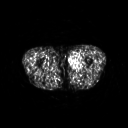
FDG PET of an extremity soft-tissue mass (from a PET/CT study), one axial slice; slice 241 of 311 in the series (ordered by position); 3.27 mm slice thickness; 128 × 128 image matrix, field of view 500 × 500 mm. Male patient, age 29 years. Case-level facts recorded for this patient, not image findings: histological type: mixoid liposarcoma; grade: low; site of the primary tumour: left thigh.
Annotated regions visible in this slice (expert contour drawn on MRI and transferred to this co-registered scan by the dataset authors):
- gross tumour volume (mass): bounding box <69,53,82,69> (left, top, right, bottom; pixels)